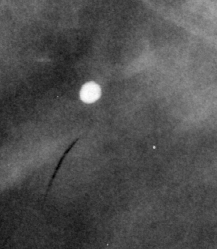
Region of interest cut from a scanned film mammogram (one marked finding); right breast; CC view.
- Finding: calcifications, morphology coarse; BI-RADS assessment category 2; subtlety rating 3 on a 1 (subtle) to 5 (obvious) scale; benign without callback (not worked up further).